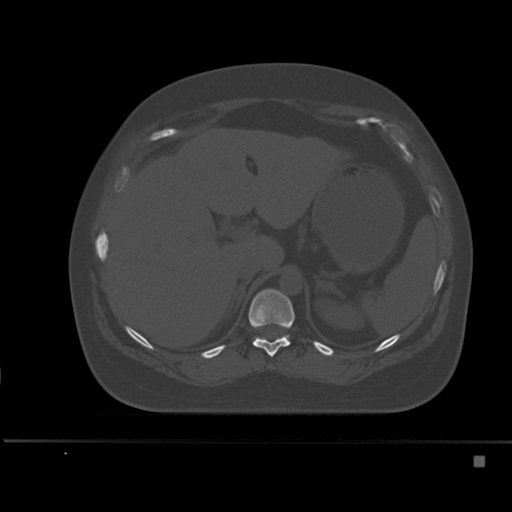
CT including the spine, one axial slice. Slice 229 of 495 in the series (ordered by position). Bone window (W 1800 / L 400 HU). 1.5 mm slice thickness. 512 × 512 image matrix, field of view 404 × 404 mm. Patient: female, 33 years. Case-level facts recorded for this patient, not image findings: primary cancer: breast; vertebrae with lytic lesions (as recorded): T1.
Outlined on this slice (semi-automatically segmented with operator editing):
- T11 vertebra: bounding box (x1, y1, x2, y2) in pixels: (248, 289, 295, 357)